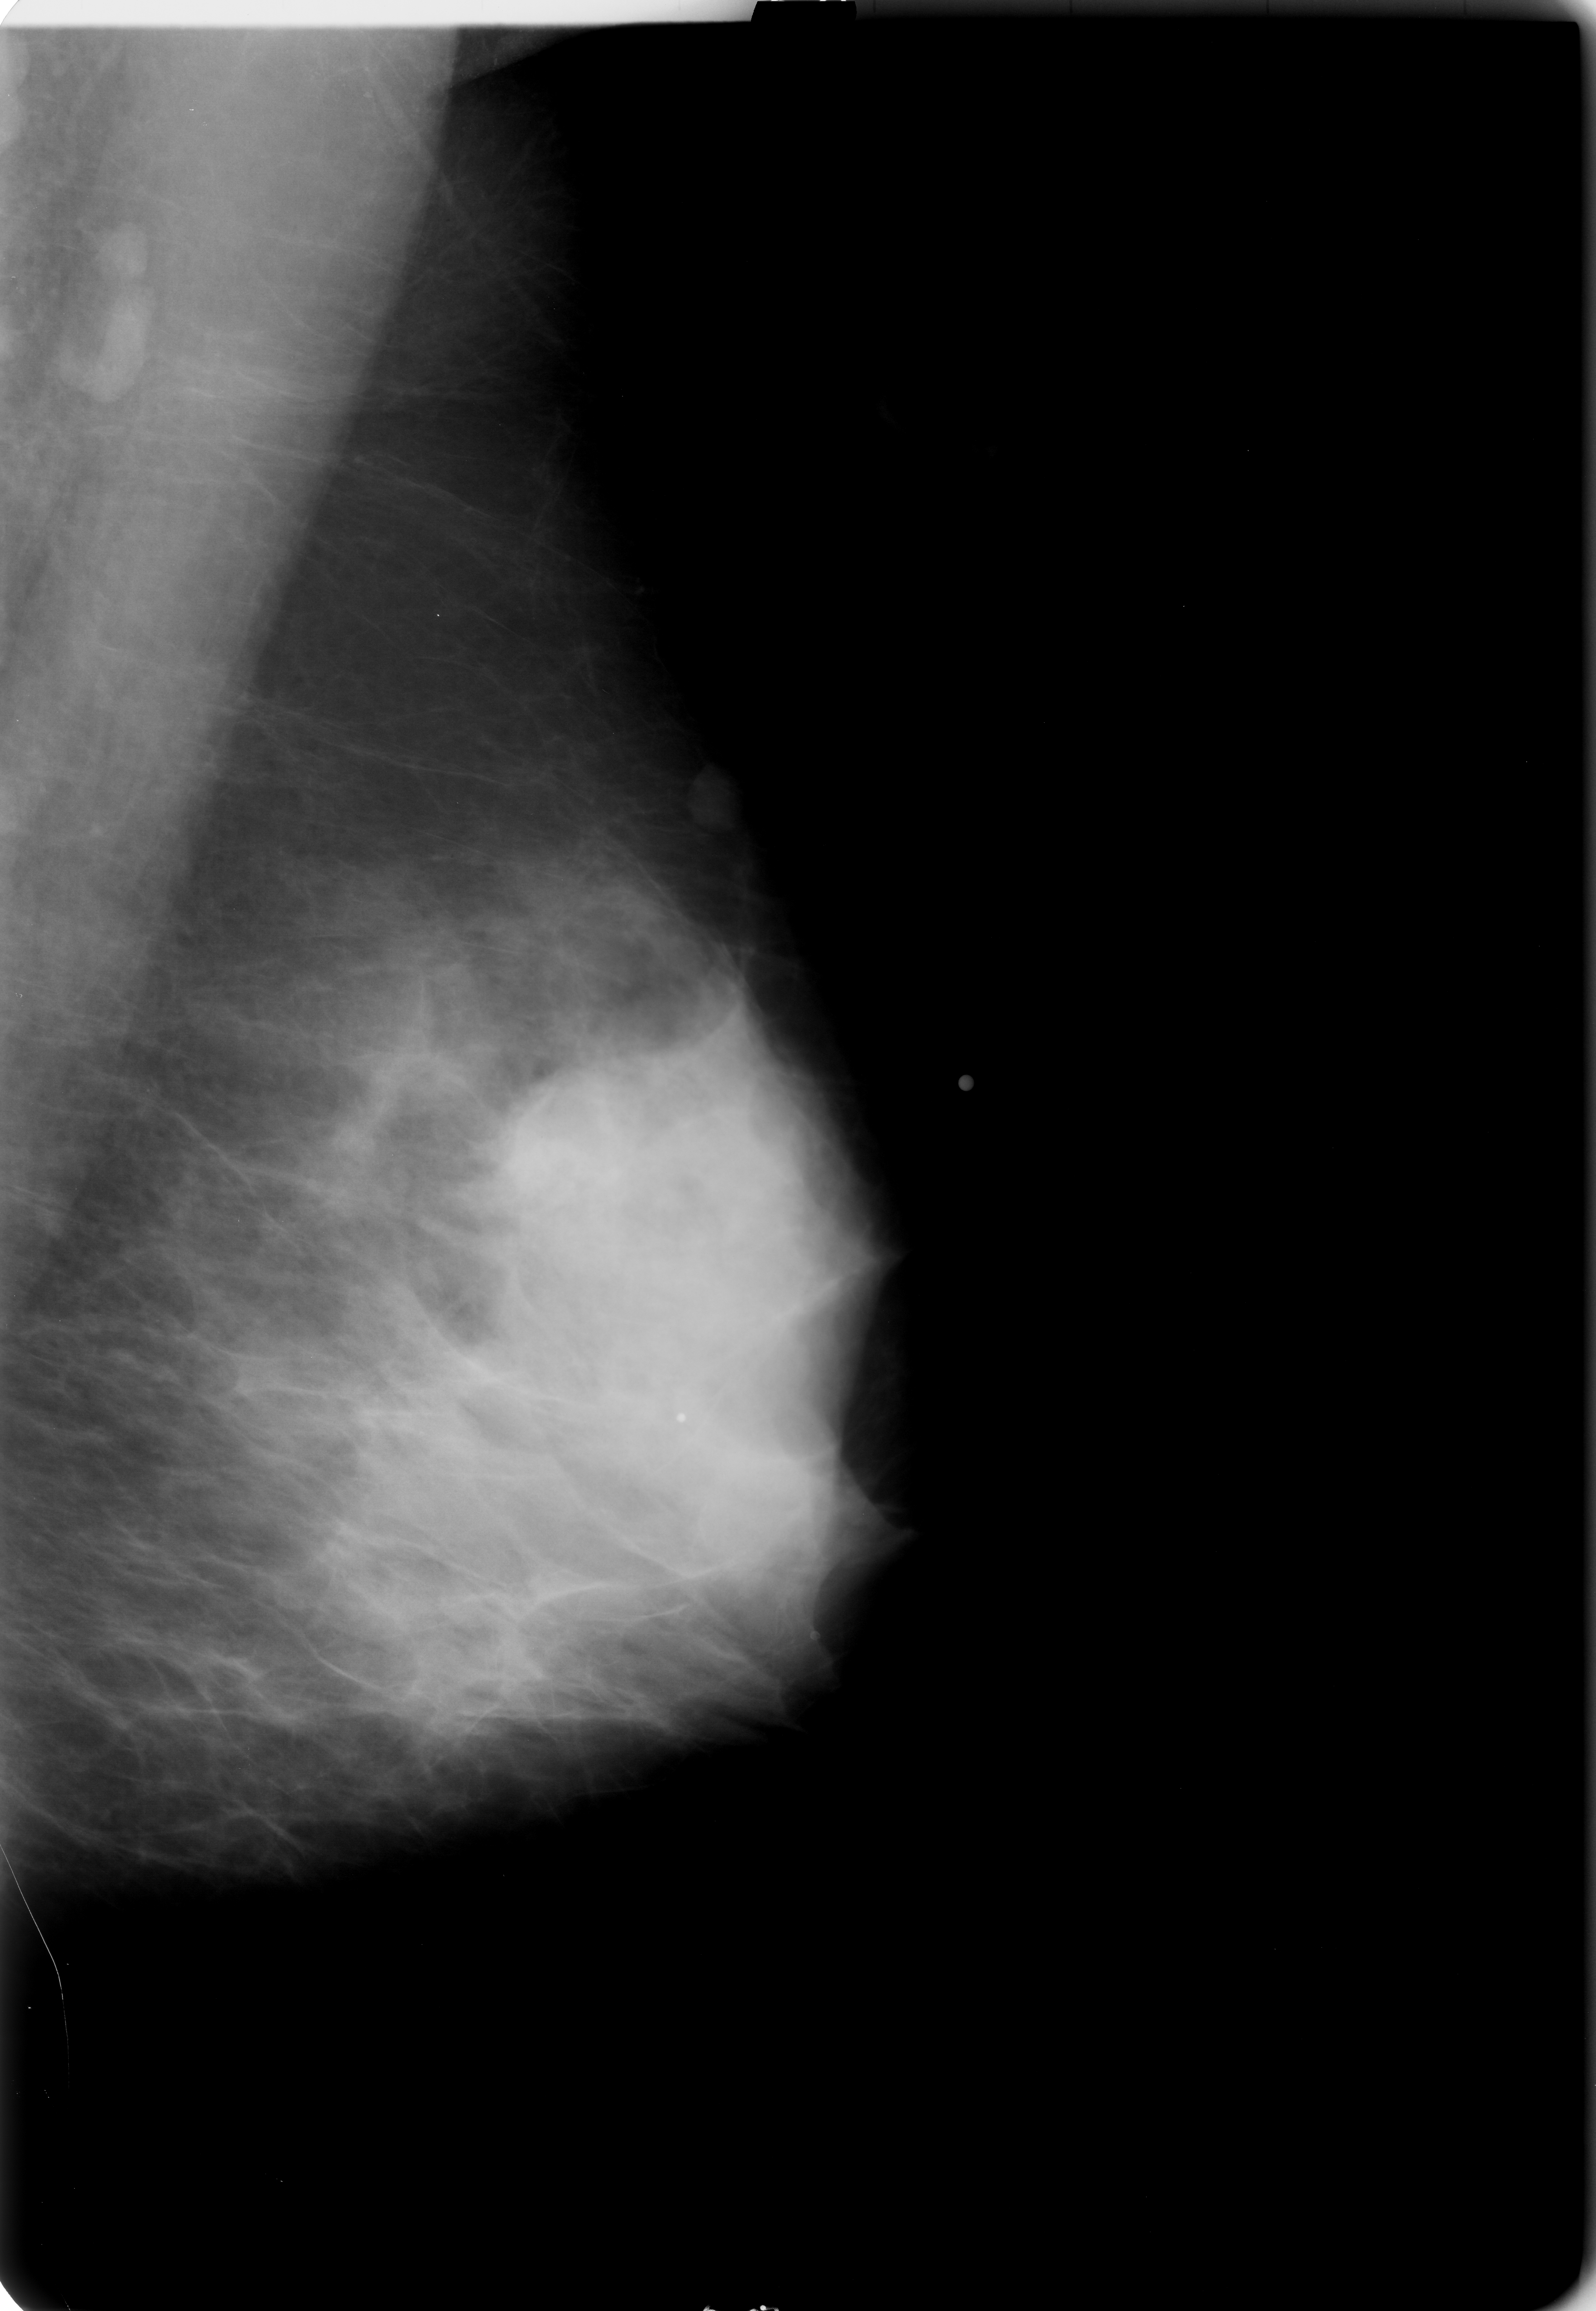
Scanned film-screen mammogram. Left breast. Mediolateral oblique (MLO) view. Breast composition: extremely dense (BI-RADS density category 4 of 4). 1596 × 2311 image matrix.
Marked abnormalities (boxes around the expert regions of interest):
- mass, shape focal asymmetric density; BI-RADS assessment category 3; subtlety rating 1 on a 1 (subtle) to 5 (obvious) scale; pathology result (as recorded, not read from the image): malignant: bounding box <481,1068,649,1261> (left, top, right, bottom; pixels)